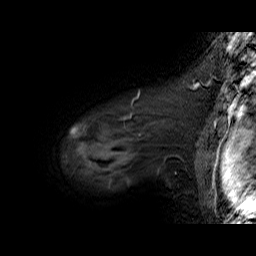
Breast MRI (dynamic contrast-enhanced), one sagittal slice; dynamic contrast-enhanced series, time point 2 of 6 at this slice position (early post-contrast); 1.5 T; TE 6.3 ms, TR 32.9 ms; 4 mm slice thickness; 256 × 256 image matrix, field of view 200 × 200 mm. Female patient. From the clinical record (not read from this slice): setting: breast cancer imaged before/during neoadjuvant chemotherapy; receptor status: HER2-positive.
Annotated regions visible in this slice (semi-automatic segmentation, software-assisted and operator-edited):
- analysis volume of interest (the breast-tissue region the enhancement analysis was run in; not a lesion): bounding box <63,92,195,174> (left, top, right, bottom; pixels)
- tumour enhancement mask (voxels above the 100 % enhancement threshold inside the analysis volume of interest): <71,96,138,133>